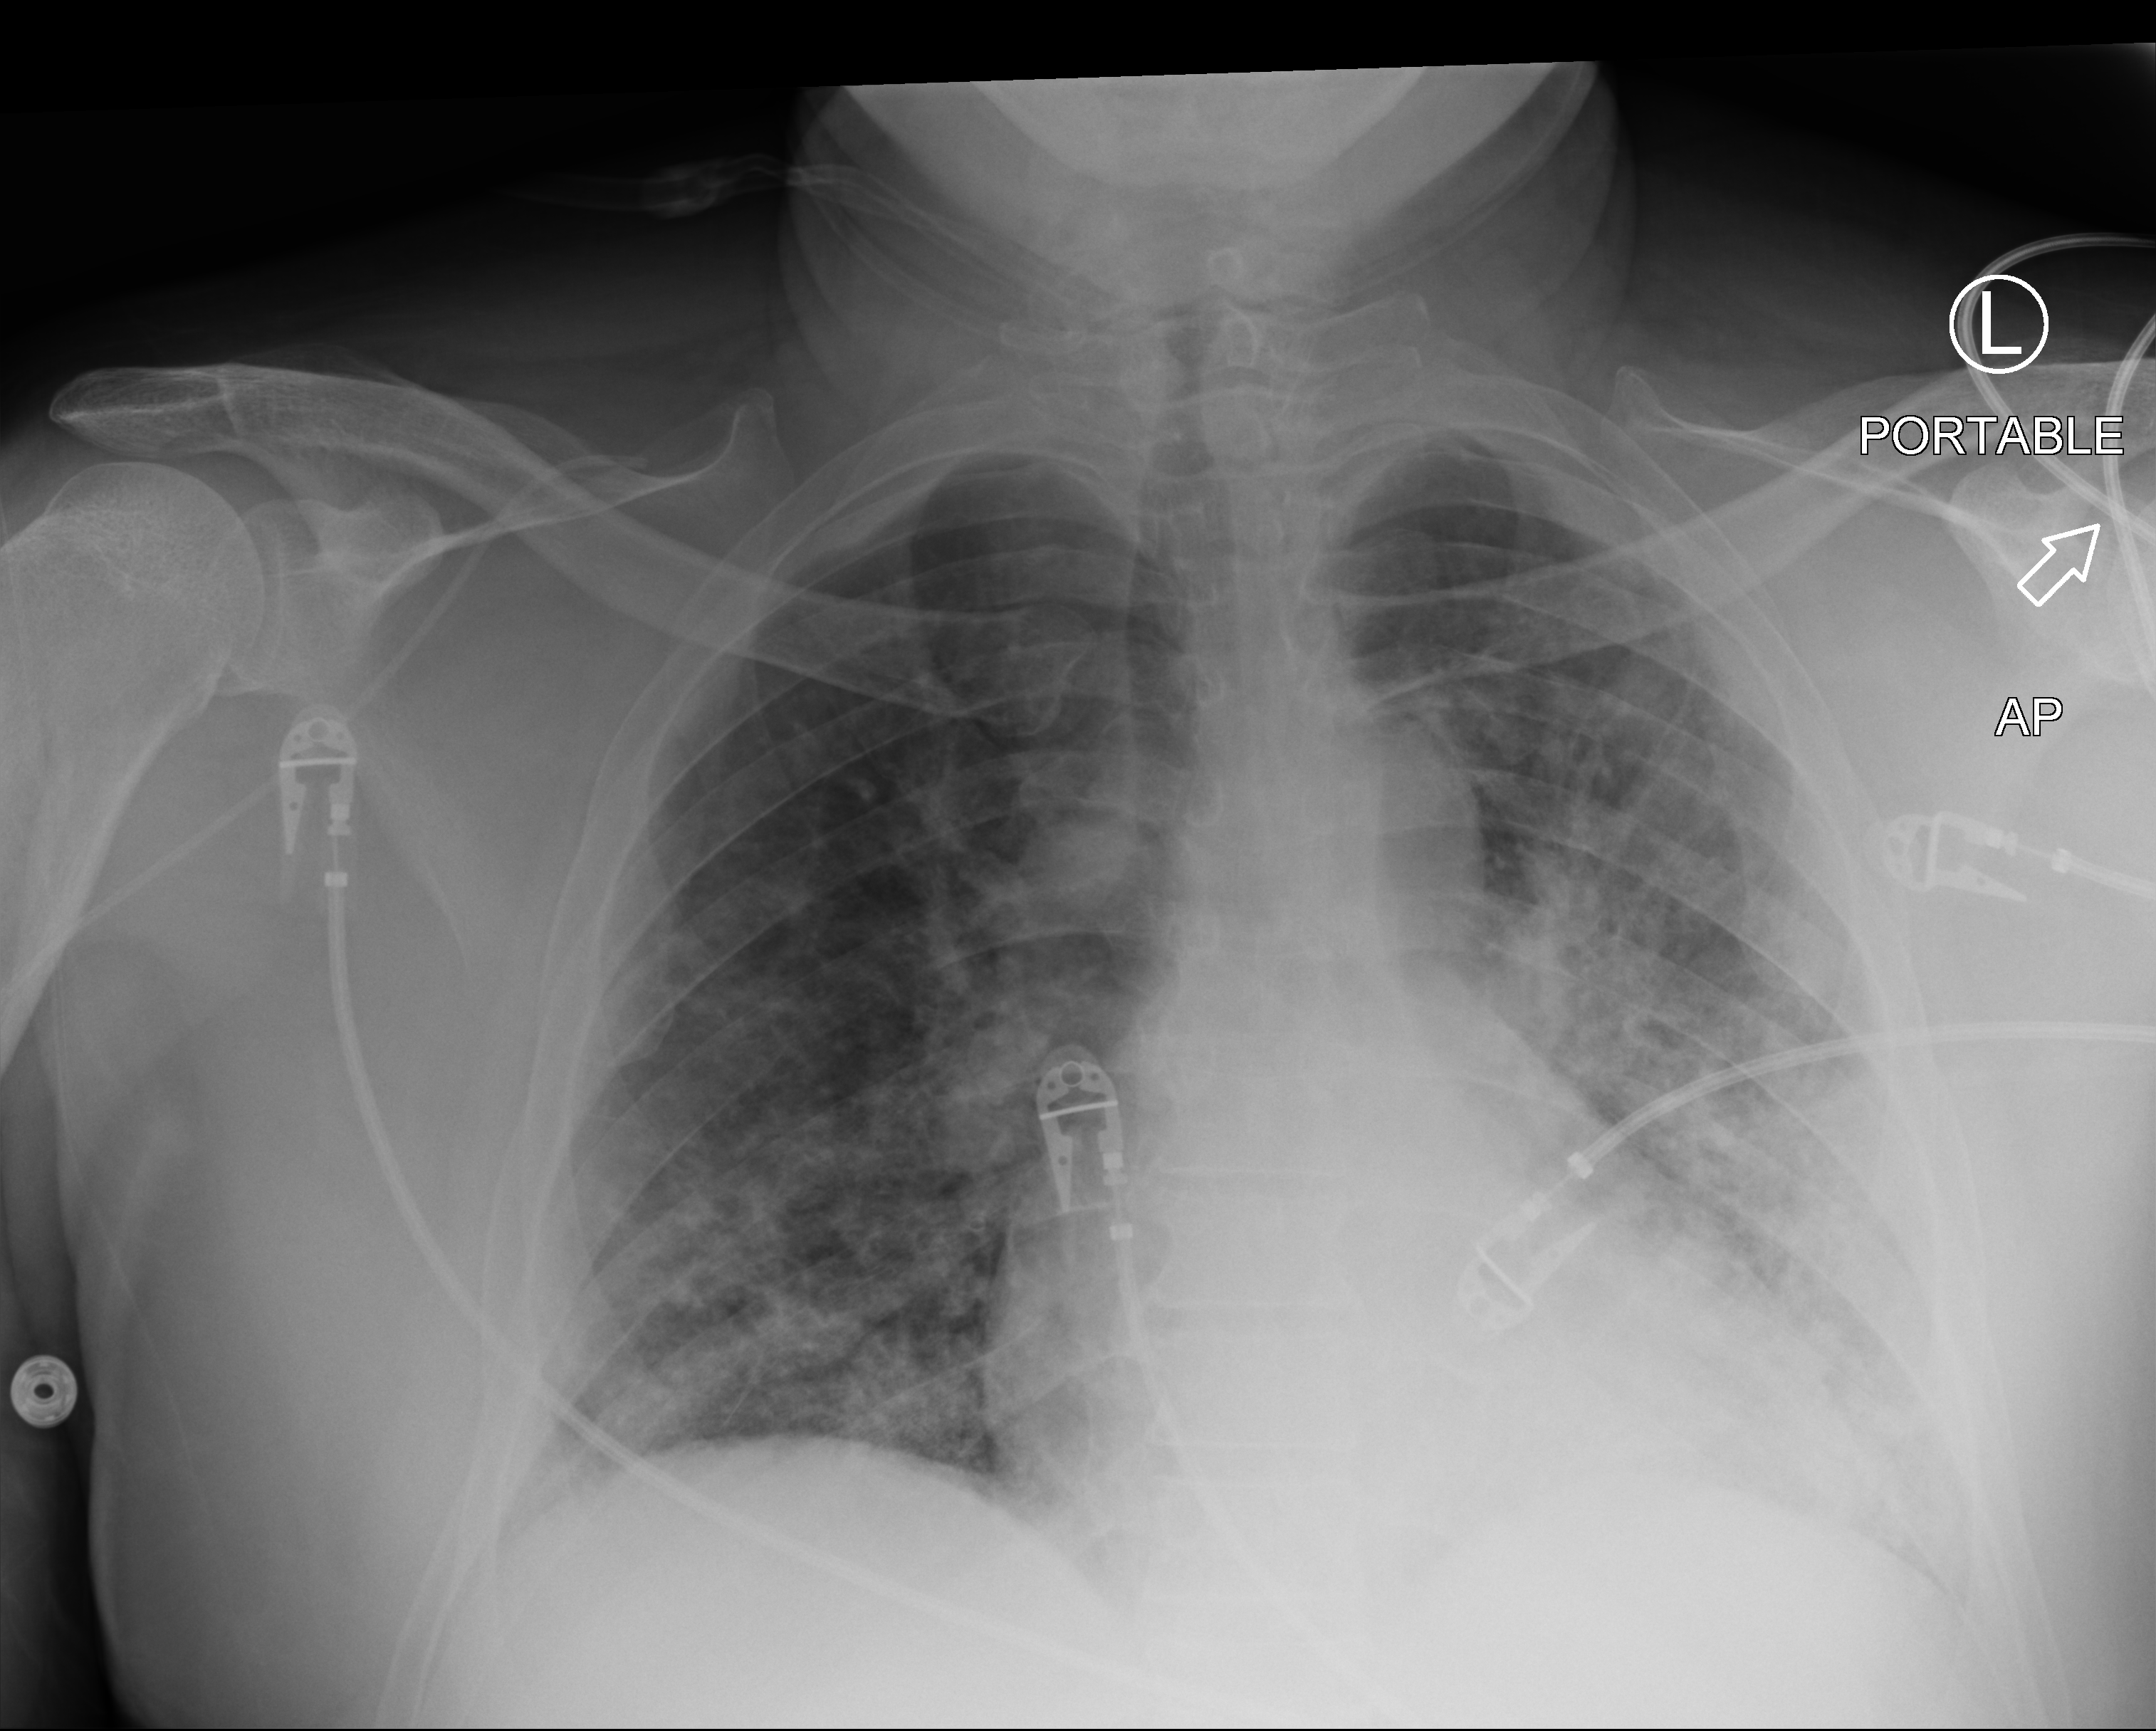
Chest X-ray (portable); anteroposterior (AP) projection. Male patient hospitalised with COVID-19, age 18–59 years.
Hospital-stay facts (about this admission, not read from this image; timing relative to this image not recorded):
- chronic kidney disease (admission record): no